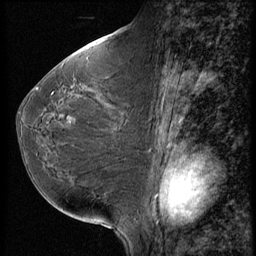
Breast MRI (dynamic contrast-enhanced), one sagittal slice. Position 28 of 56 along the scan axis. 3 images stored at this slice position (order not interpretable as contrast timing). 1.5 T. TE 4.2 ms, TR 9 ms. 2.5 mm slice thickness. 256 × 256 image matrix, field of view 180 × 180 mm. Patient: female, 49 years. Case-level facts recorded for this patient, not image findings: setting: breast cancer imaged before/during neoadjuvant chemotherapy; receptor status: HER2-positive.
Outlined on this slice (semi-automatically segmented with operator editing):
- analysis volume of interest (the breast-tissue region the enhancement analysis was run in; not a lesion): bounding box <17,74,148,198> (left, top, right, bottom; pixels)
- tumour enhancement mask (voxels above the 140 % enhancement threshold inside the analysis volume of interest): <38,89,76,122>